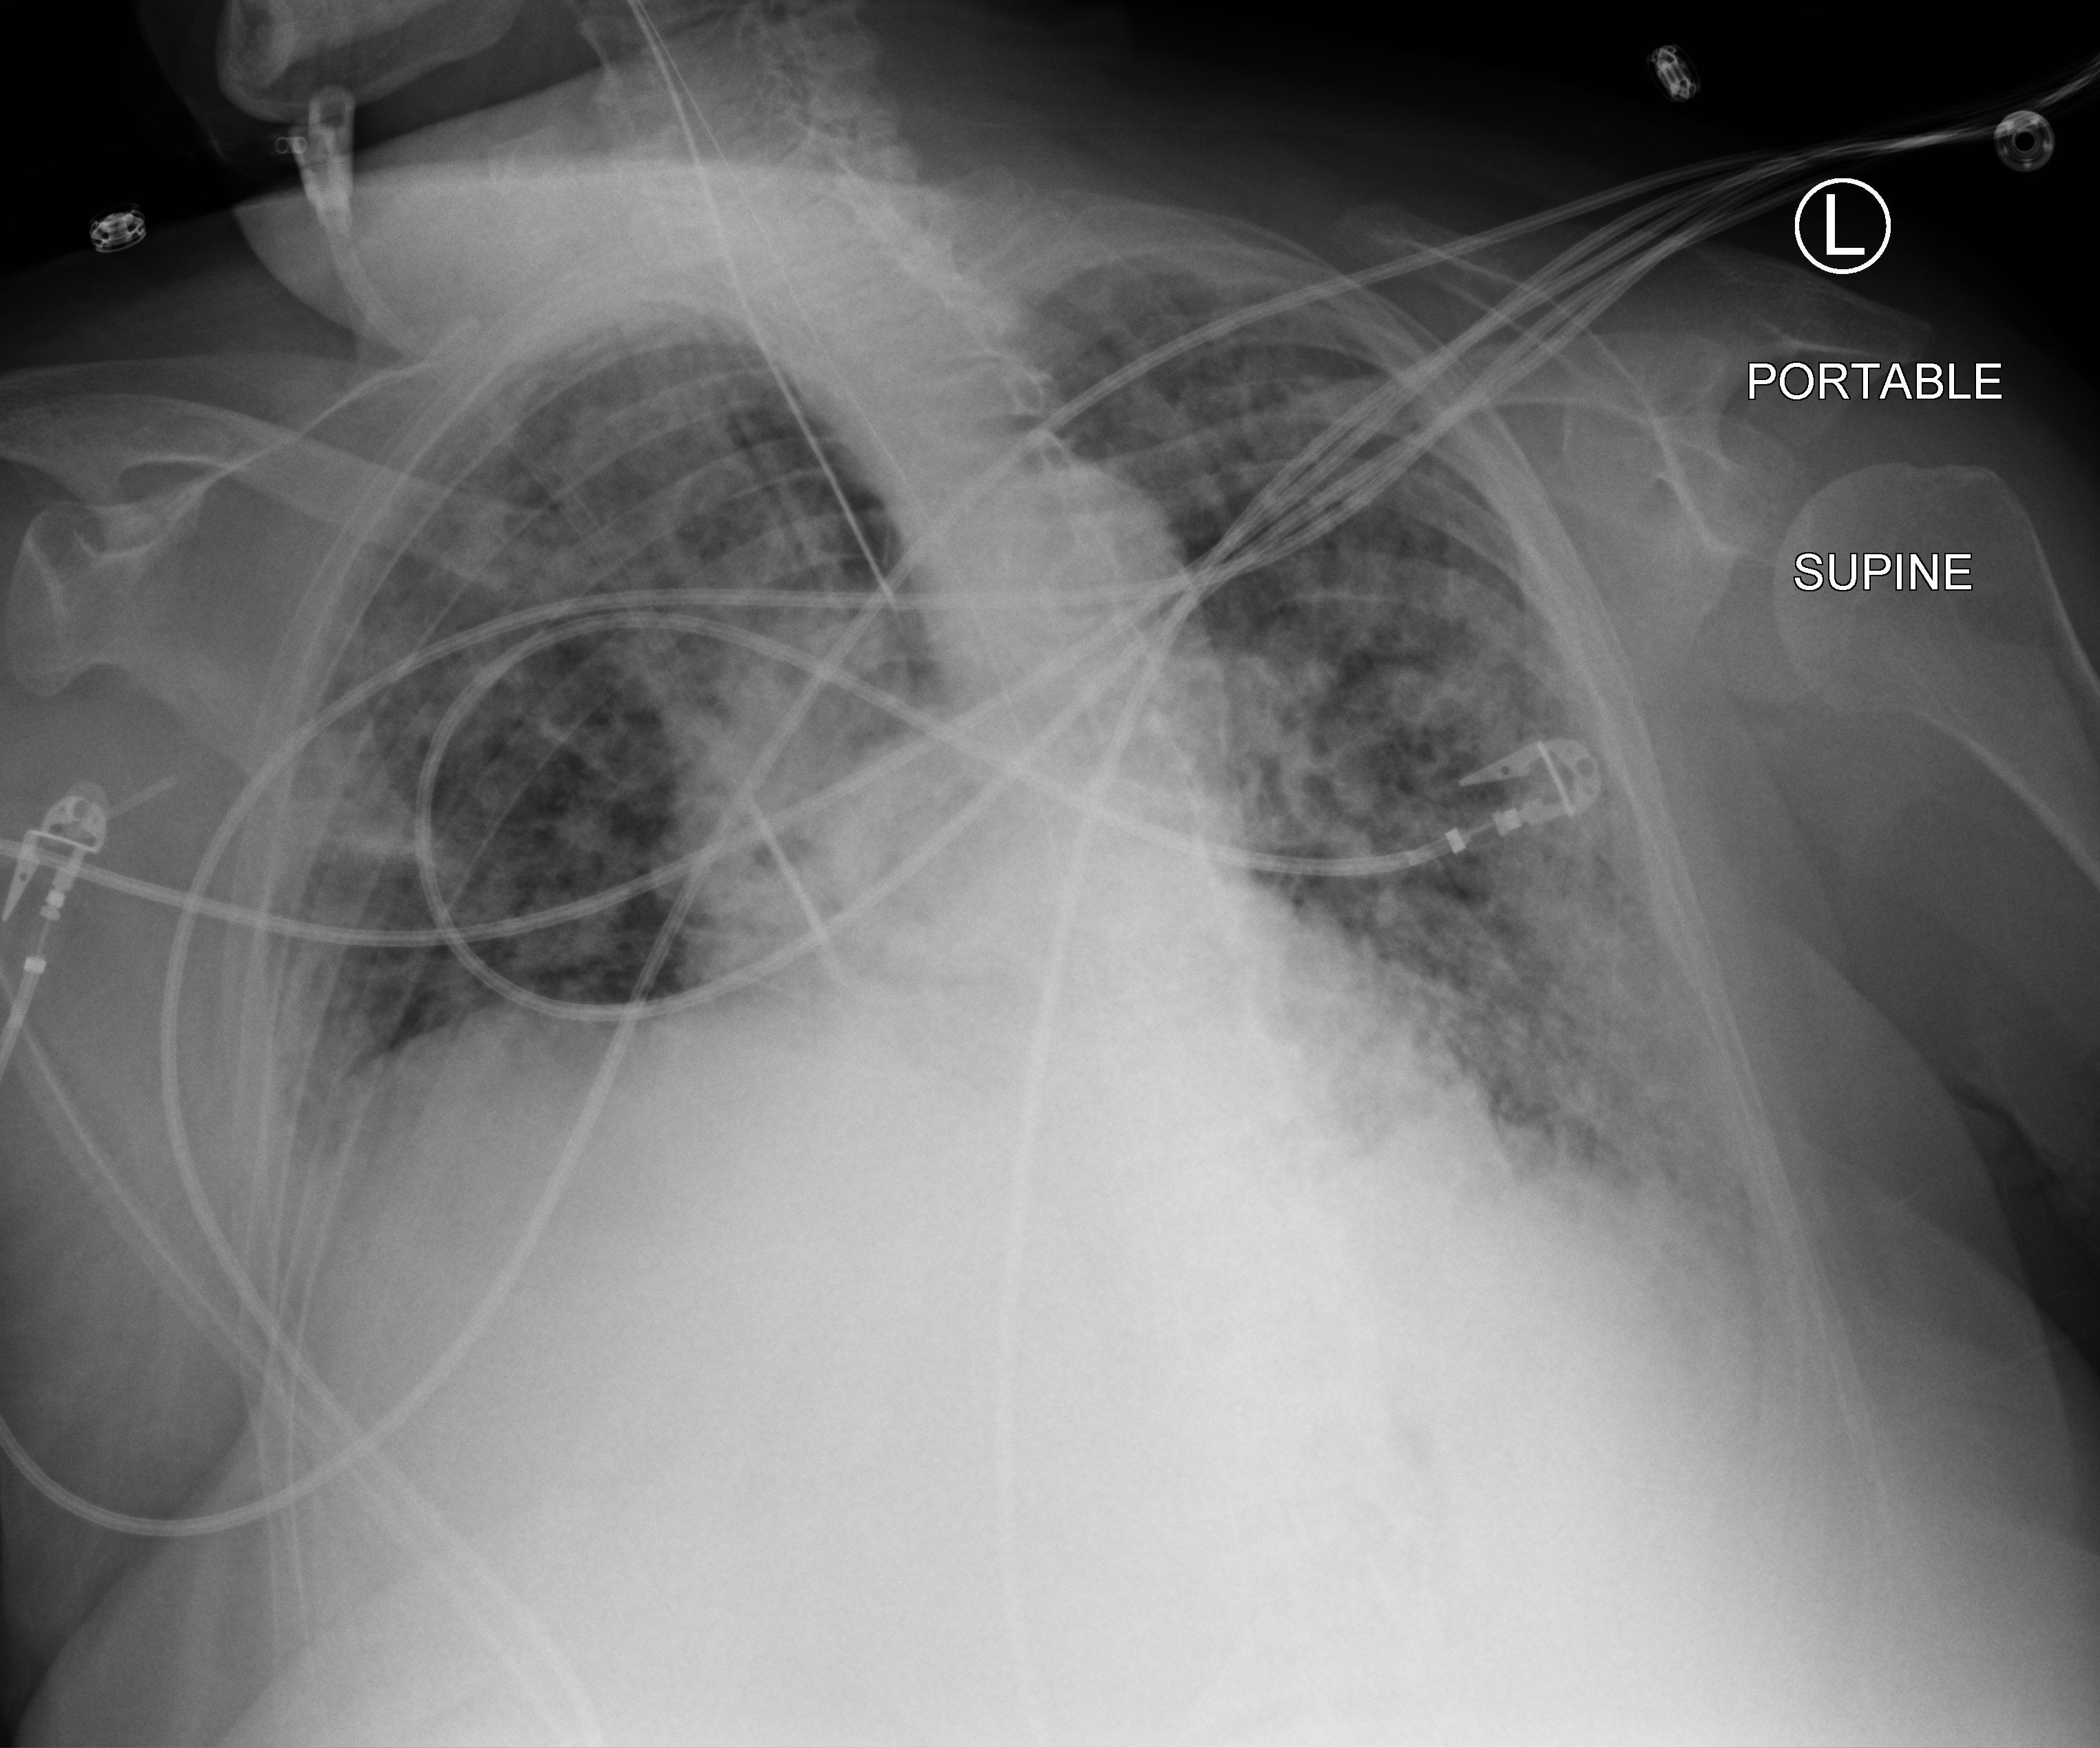
Portable chest radiograph, anteroposterior (AP) projection. Patient hospitalised with COVID-19; female, aged 75–90 years.
Hospital-stay facts (about this admission, not read from this image; timing relative to this image not recorded): mechanically ventilated during this hospital stay: yes; admitted to intensive care during this hospital stay: yes; smoking status (admission record): former.